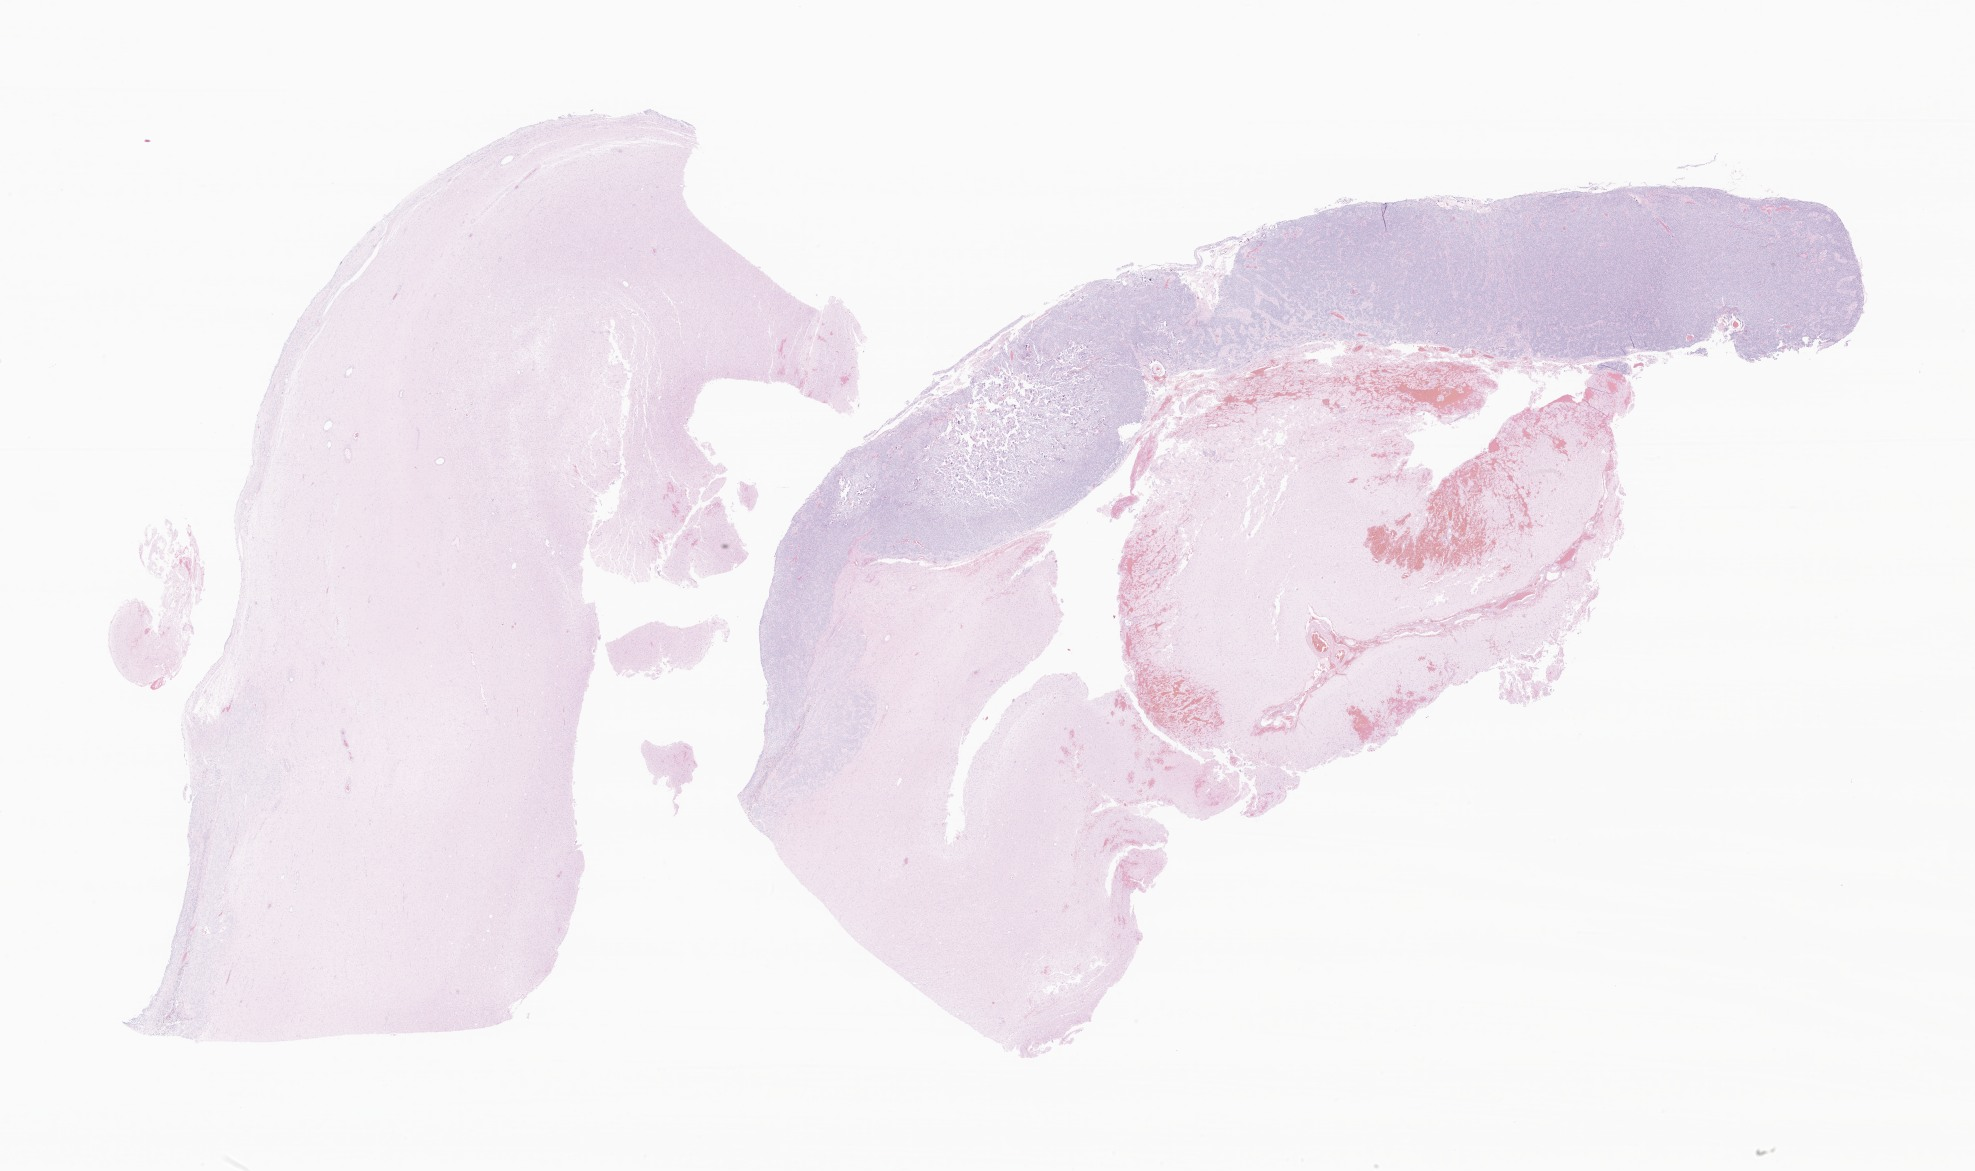
Digitized H&E-stained section of tumor tissue from the brain, whole scanned area (about 33.3 x 19.8 mm) shown as a low-resolution overview; formalin-fixed paraffin-embedded section. Patient: female, age 674 days (about 1.8 years).
Diagnosis: Ependymoma, NOS.